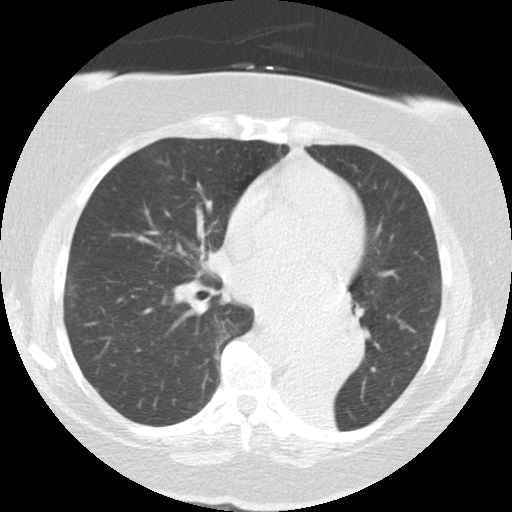
Chest CT (low-dose screening protocol), one axial image; first (baseline) screen; lung window (W 1500 / L -600 HU); 2.5 mm slice thickness; standard (soft-tissue) reconstruction kernel (STANDARD). Female participant, aged 71 years at enrolment.
Lesion marked by an expert reader, bounding box <284,305,366,383> (left, top, right, bottom; pixels). The exam's reader record, not a measurement of the box and not confirmed to be the same lesion: non-calcified nodule or mass ≥4 mm, right middle lobe, 5 × 5 mm, smooth margins, soft tissue attenuation. Note: the box lies in the patient's left hemithorax on this image, whereas the reader's record names the right lung; they may be different findings.